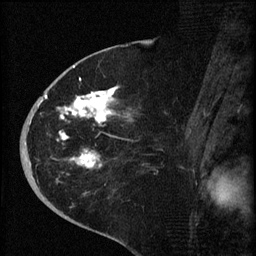
Breast MRI (dynamic contrast-enhanced), one sagittal slice; position 34 of 60 along the scan axis; dynamic contrast-enhanced series, image 2 of 4 at this slice position (ordered by acquisition); 1.5 T; TE 4.2 ms, TR 8.2 ms; 256 × 256 image matrix. Female patient, age 71 years.
Structures marked on this image (semi-automatic segmentation, software-assisted and operator-edited):
- analysis volume of interest (the breast-tissue region the enhancement analysis was run in; not a lesion): bounding box [x1, y1, x2, y2] px = [35, 75, 142, 190]
- tumour enhancement mask (voxels above the 70 % enhancement threshold inside the analysis volume of interest): [38, 77, 129, 168]